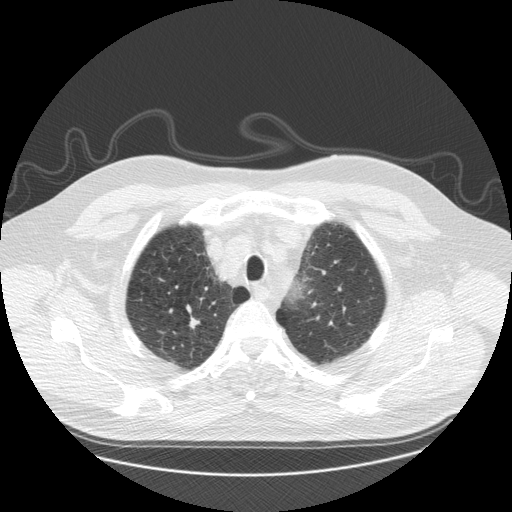
Low-dose screening chest CT, one axial slice; slice 146 of 173 in the series (ordered by position); reconstruction kernel STANDARD; lung window (W 1500 / L -600 HU); 2.5 mm slice thickness; 512 × 512 image matrix, field of view 400 × 400 mm.
Annotated regions visible in this slice (manually delineated by an expert):
- lesion 1 (tumor, upper lobe of right lung): bounding box (x1, y1, x2, y2) in pixels: (190, 317, 200, 329)